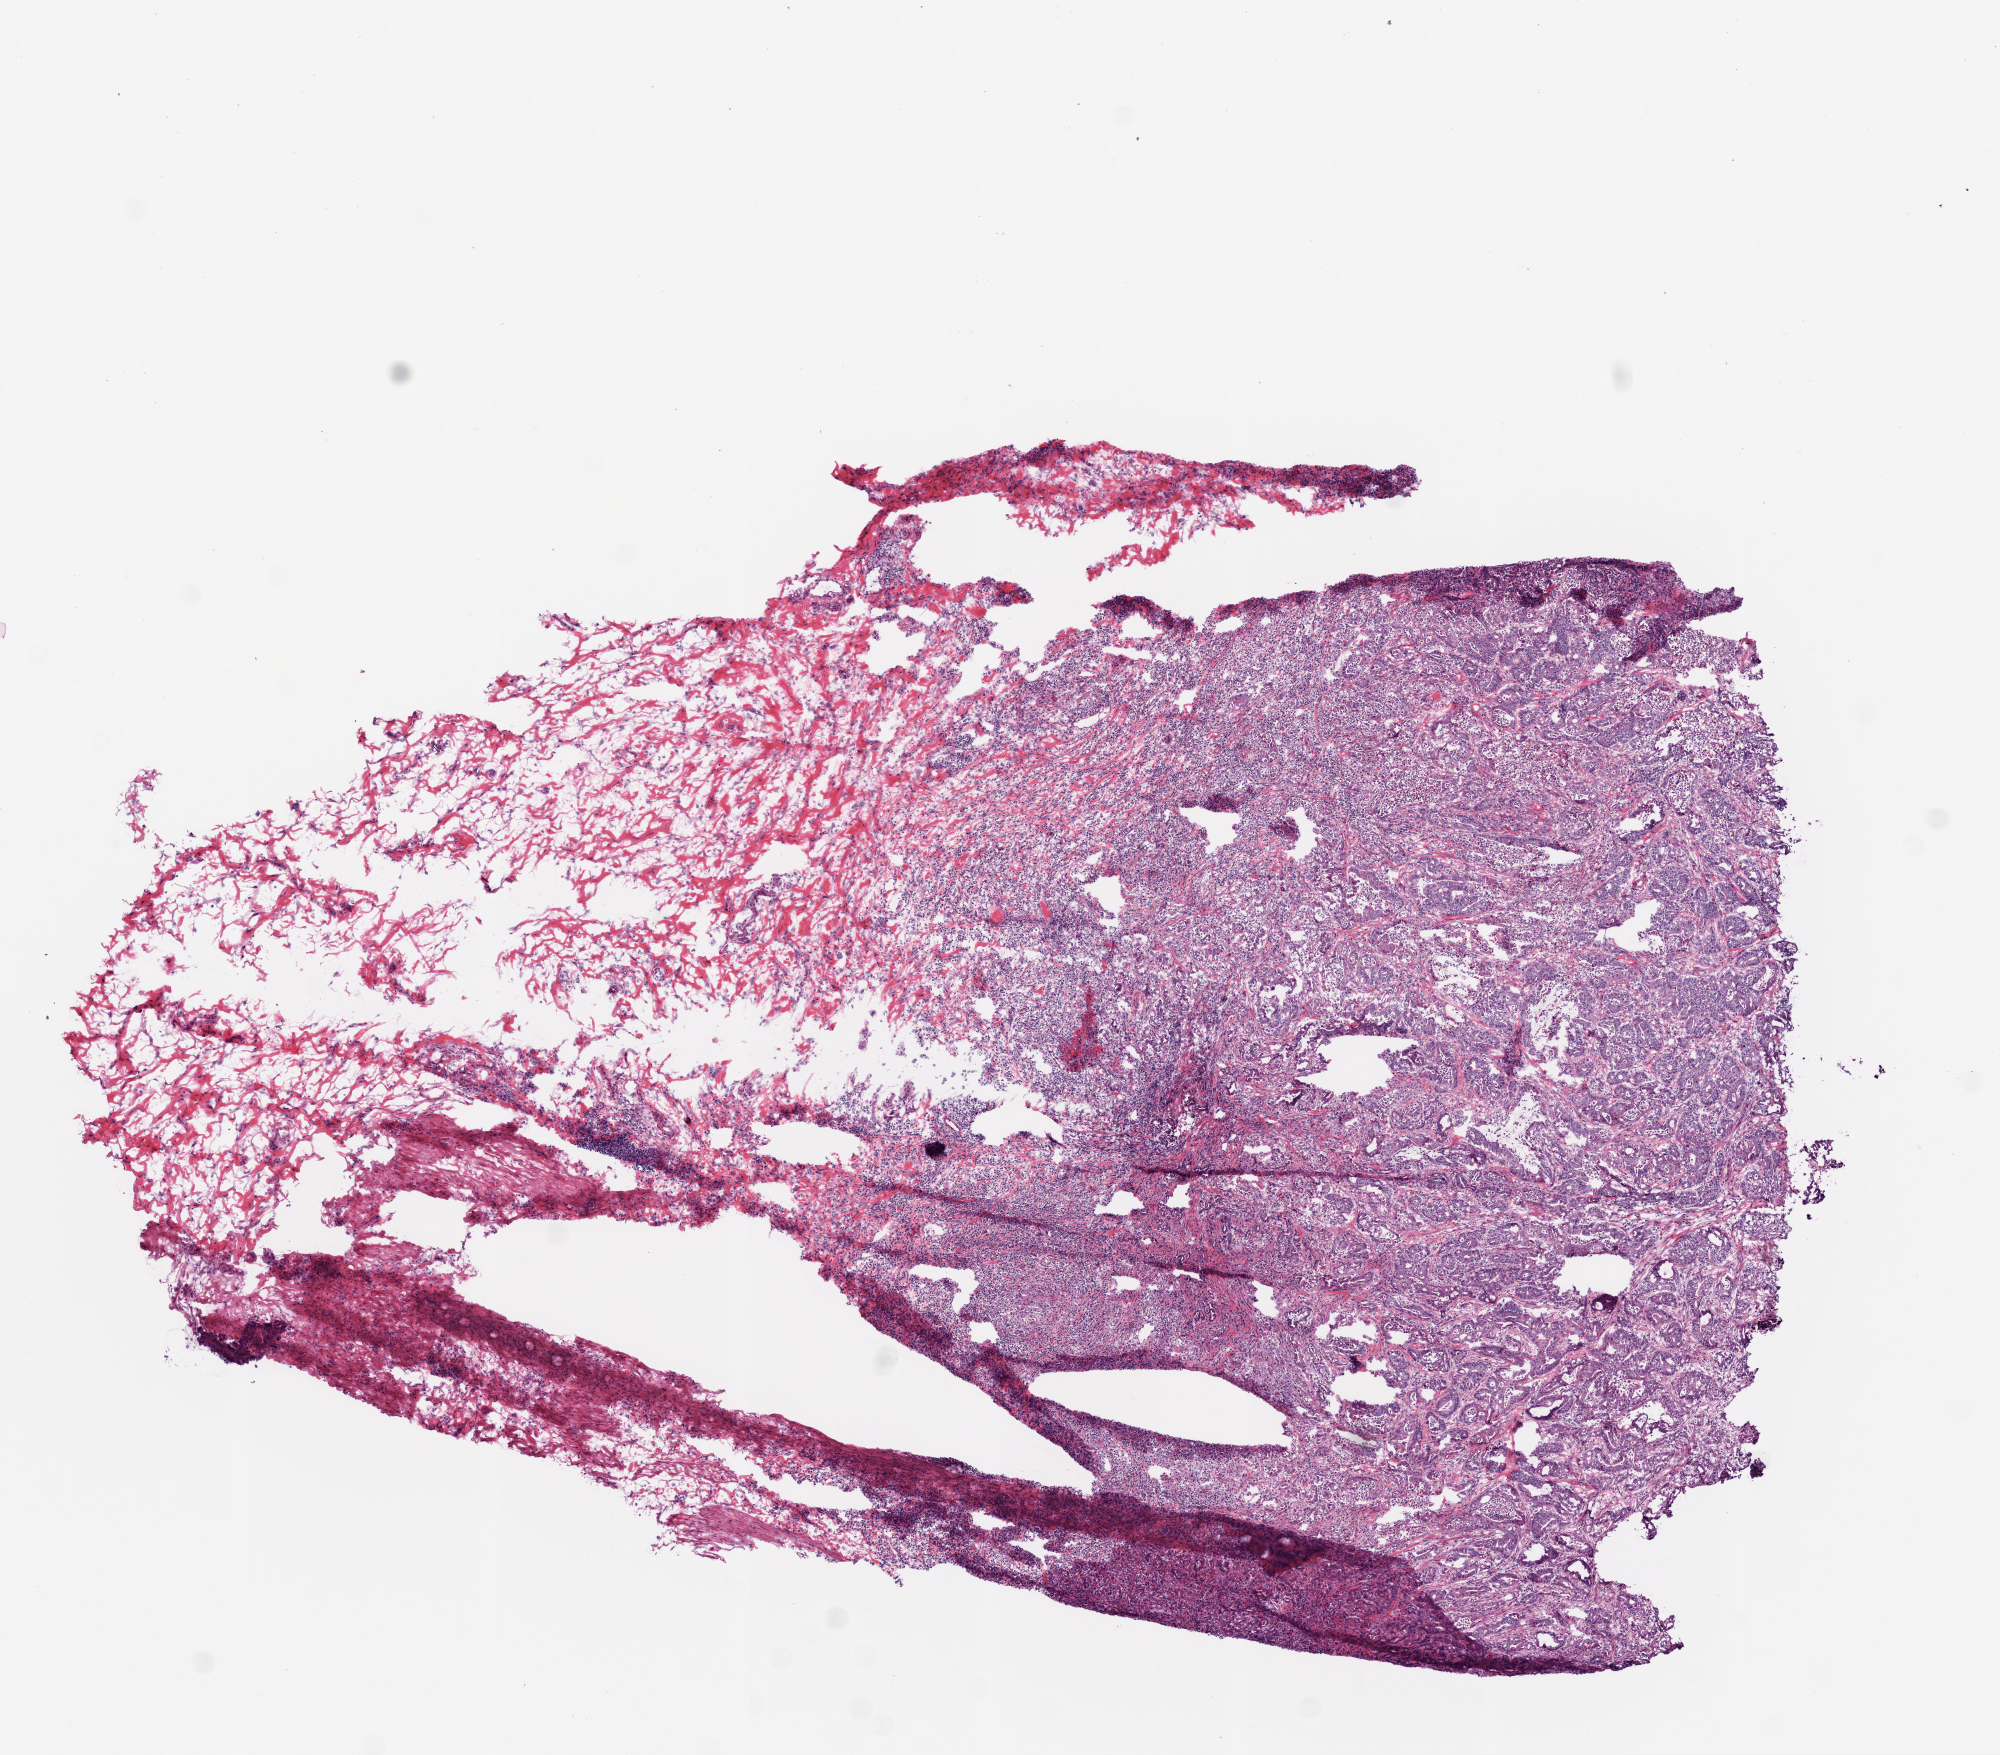
Digitized H&E tissue section (whole slide) — low-resolution overview of the scanned area, about 8.0 x 7.0 mm (slide scanned at 20x). Frozen section. Sample: primary tumour, colon. Patient: female, age at initial diagnosis 62 years. Slide review estimates, as recorded: tumour cells 60%, tumour nuclei 90%, normal cells 0%, stromal cells 40%, necrosis 0%.
- TNM: T3 N0 M0
- lymph nodes positive (case pathology): 0 of 39 examined
- AJCC pathologic stage: IIA (6th edition)
- pathologic diagnosis: Adenocarcinoma, NOS (ascending colon)